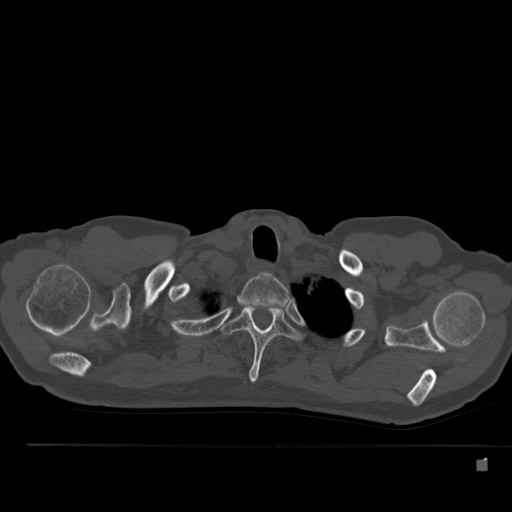
CT including the spine, one axial slice; slice 416 of 517 in the series (ordered by position); bone window (W 1800 / L 400 HU); 512 × 512 image matrix. Patient: male, 70 years. From the clinical record (not read from this slice): primary cancer: renal.
Annotated regions visible in this slice (semi-automatic segmentation, software-assisted and operator-edited):
- T1 vertebra: bounding box <242,273,289,305> (left, top, right, bottom; pixels)
- T2 vertebra: <222,303,300,383>